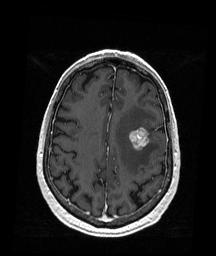
Brain MRI from a brain-tumour surgery series, one axial slice. Position 62 of 176 along the scan axis. T1-weighted post-contrast. 216 × 256 image matrix. From the clinical record (not read from this slice): histopathology: Metastatic Melanoma; tumour location: Left Frontal.
Outlined on this slice (manually delineated by an expert):
- tumour: bounding box (x1, y1, x2, y2) in pixels: (129, 128, 151, 149)